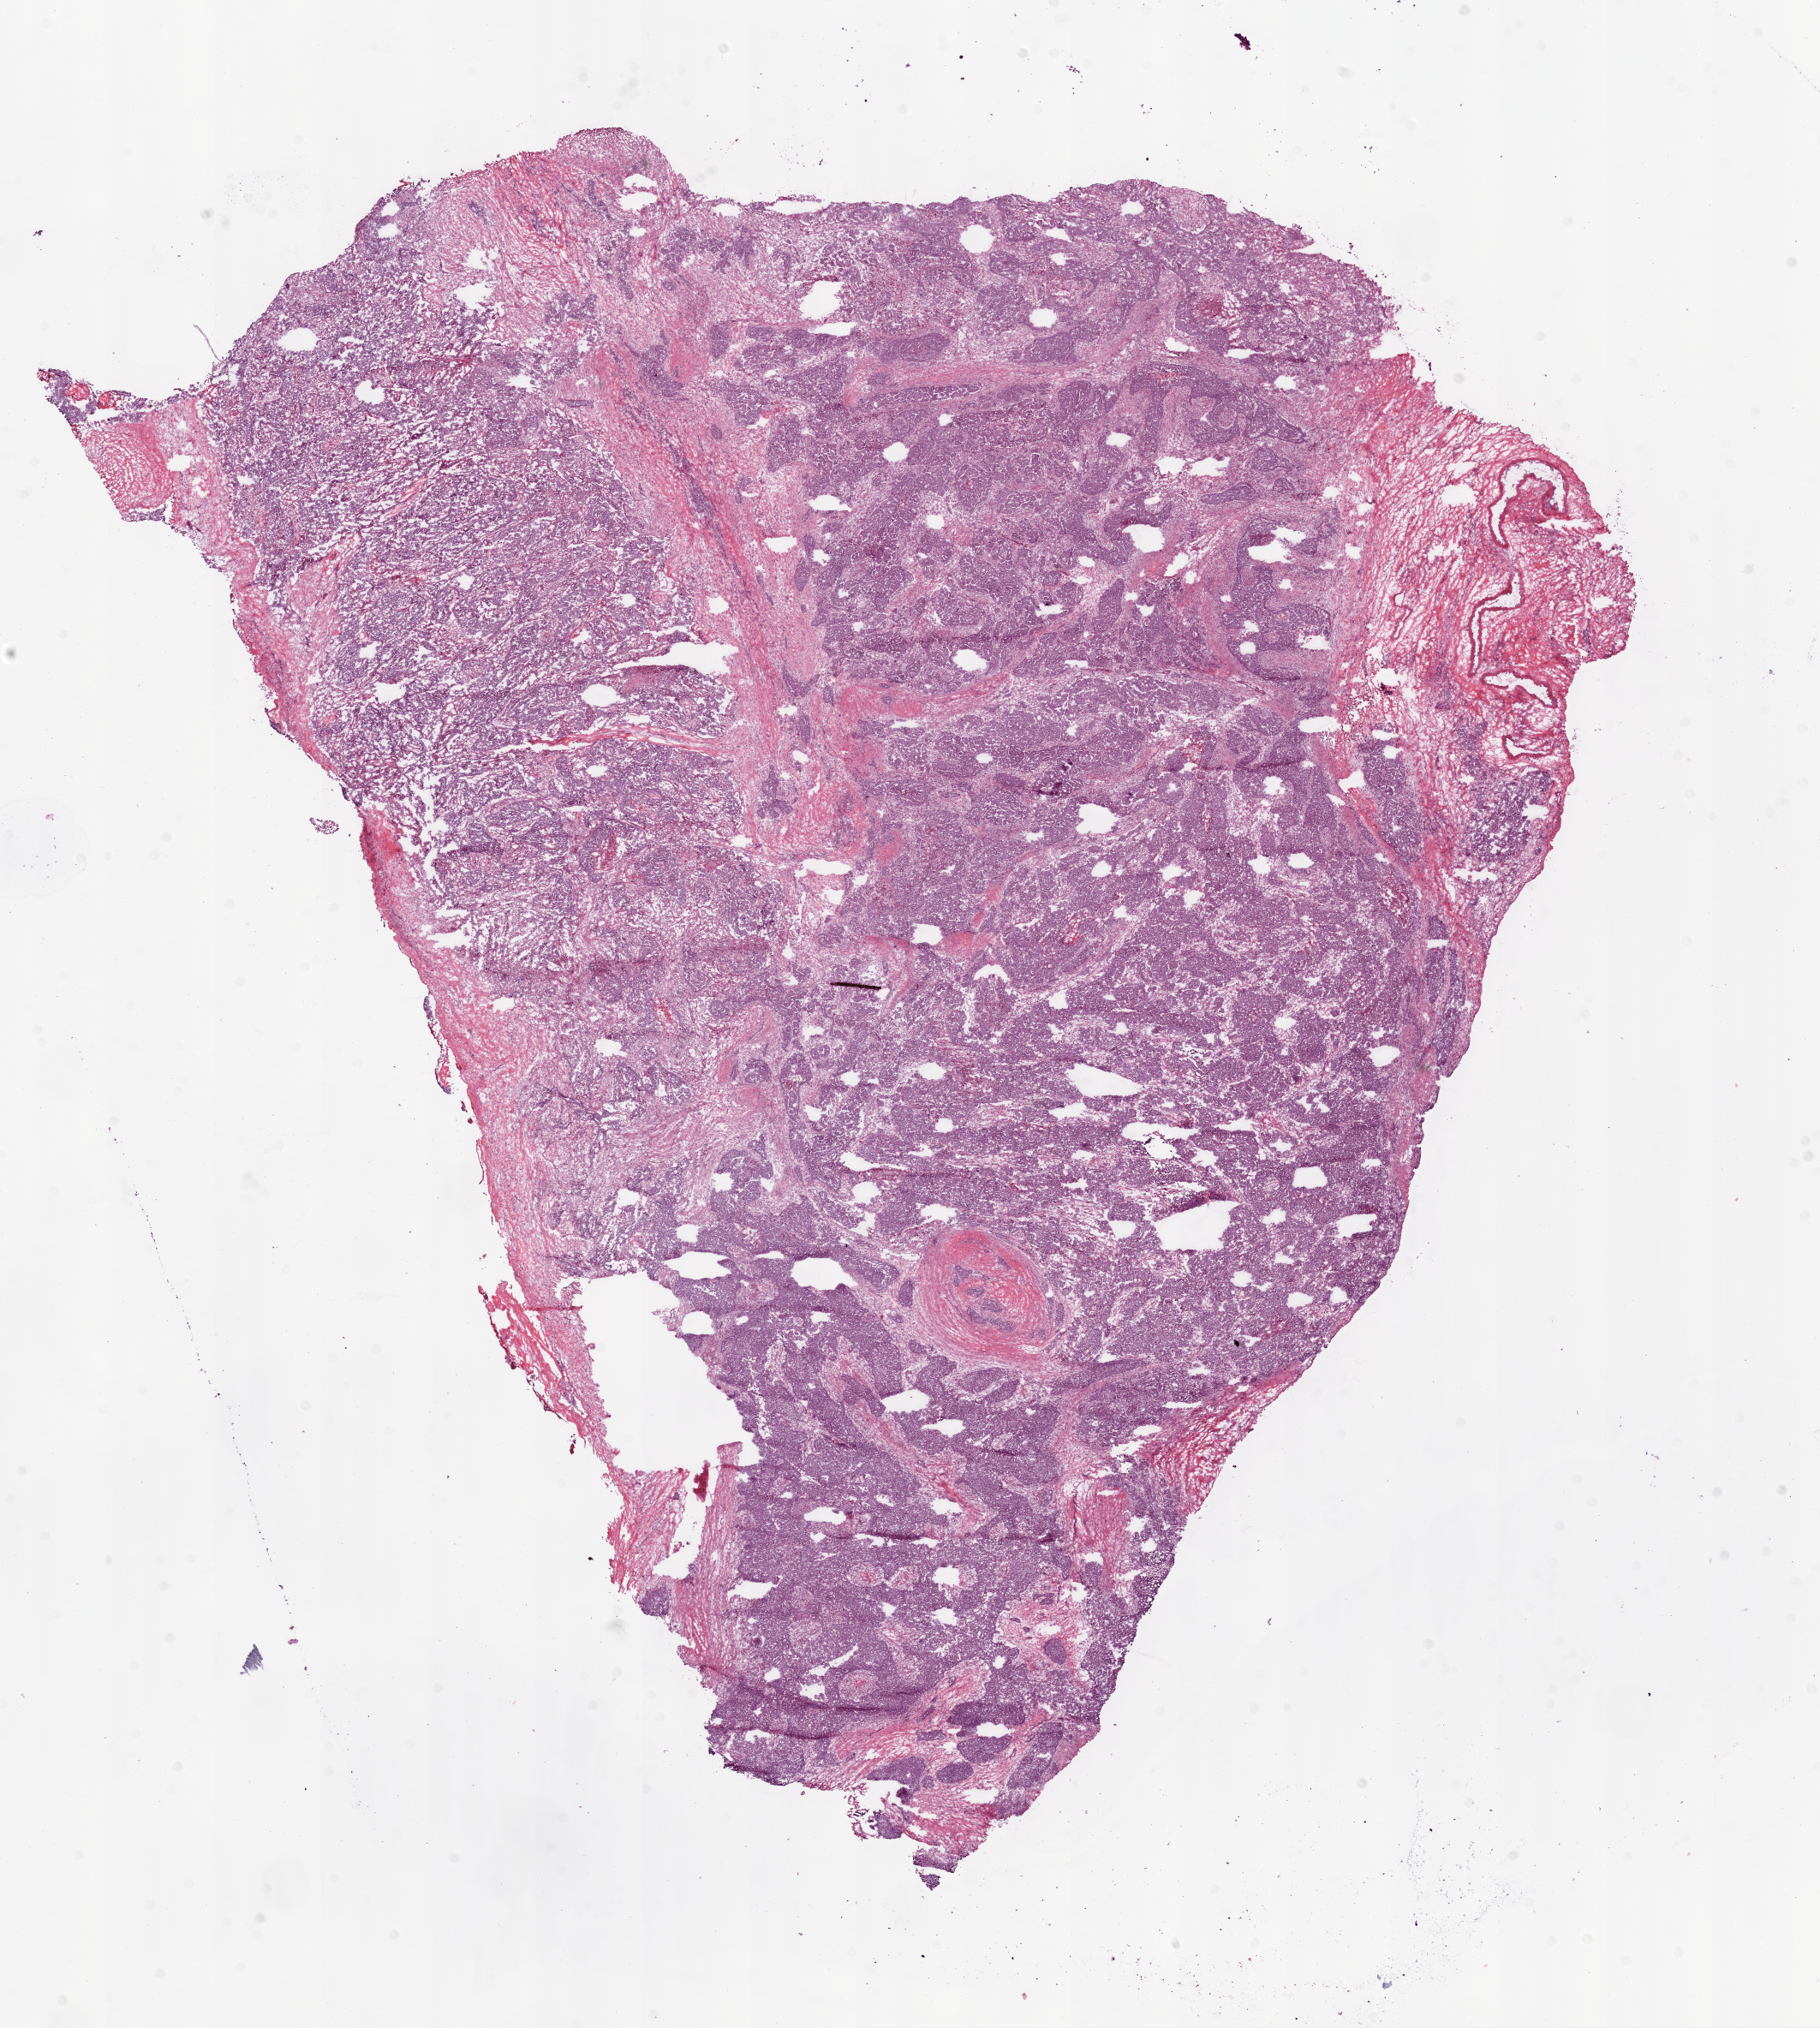
Digitized H&E tissue section (whole slide) — low-resolution overview of the scanned area, about 17.1 x 19.0 mm; frozen section from the bottom of the tissue portion; ovary, primary tumour sample. Female, age 58 years at initial diagnosis. Histologic grade: G2 (moderately differentiated). Pathologist review of this section (percent, as recorded): tumour cells 75%, tumour nuclei 80%, normal cells 0%, stromal cells 20%, necrosis 5%.
- FIGO stage: IIIC
- diagnosis: Serous cystadenocarcinoma, NOS